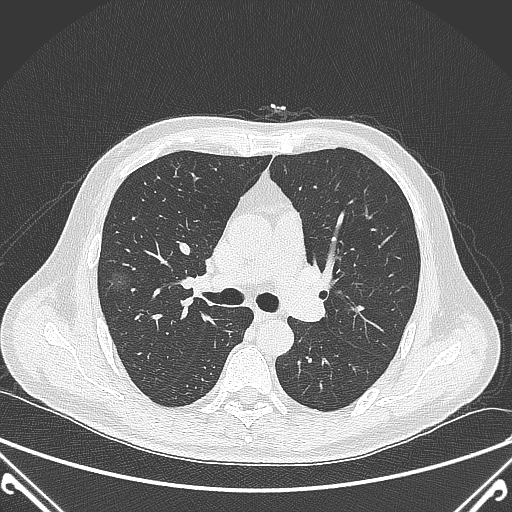
Chest CT, one axial slice. Position 229 of 360 along the scan axis. Lung window (W 1500 / L -600 HU). 1 mm slice thickness. 512 × 512 image matrix, field of view 380 × 380 mm. Male patient, age 64 years. From the clinical record (not read from this slice): clinical TNM (as recorded): T1c N0 M0; histopathological grade: G2.
Outlined on this slice (bounding box drawn by a radiologist):
- lung tumour (recorded histology: adenocarcinoma): bounding box <101,262,134,302> (left, top, right, bottom; pixels)